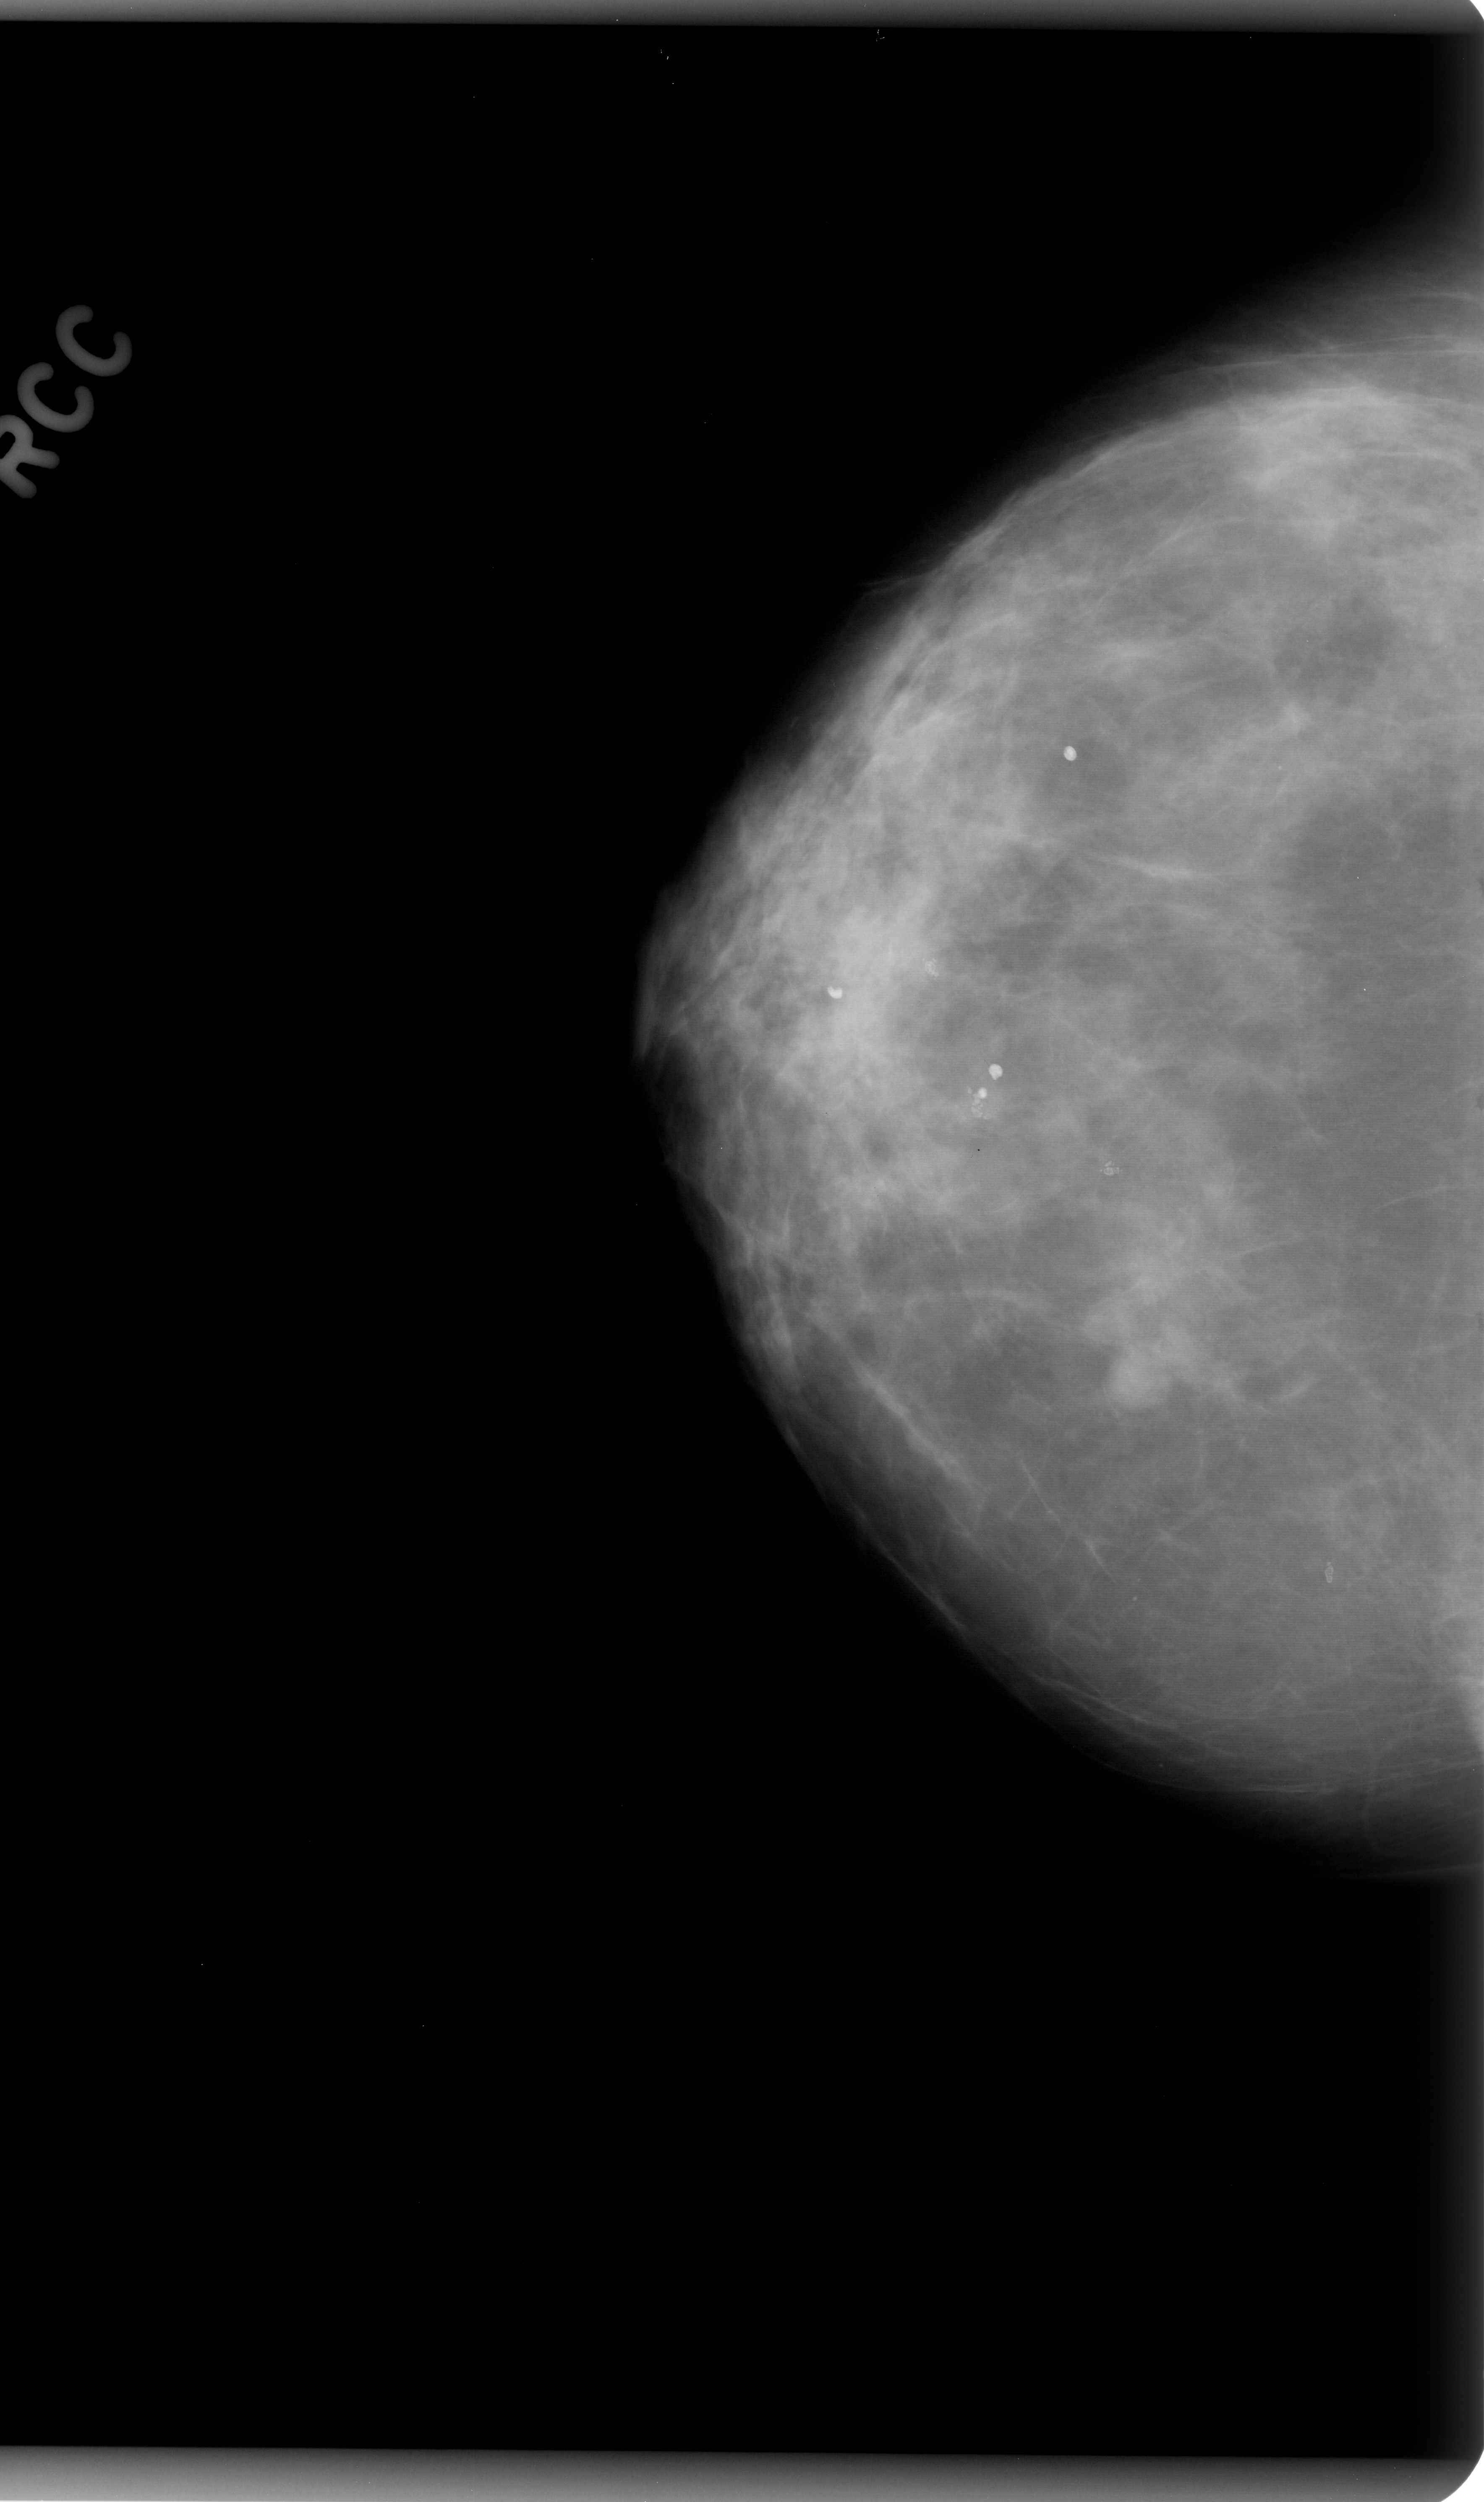
Mammogram (digitized film); right breast; craniocaudal (CC) view; BI-RADS breast density category 2 (scale 1–4).
- Finding: mass, shape round, margins circumscribed; BI-RADS assessment category 3; pathology (as recorded): benign.